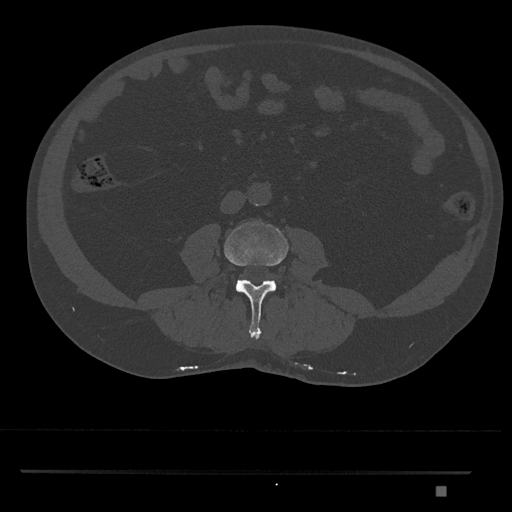
CT including the spine, one axial slice. Slice 669 of 1134 in the series (ordered by position). Reconstruction kernel Br40s/3. Bone window (W 1800 / L 400 HU). 0.5 mm slice thickness. 512 × 512 image matrix. Patient: male, 65 years. Case-level facts recorded for this patient, not image findings: primary cancer: prostate.
Annotated regions visible in this slice (semi-automatic segmentation, software-assisted and operator-edited):
- L3 vertebra: bounding box <224,221,289,340> (left, top, right, bottom; pixels)